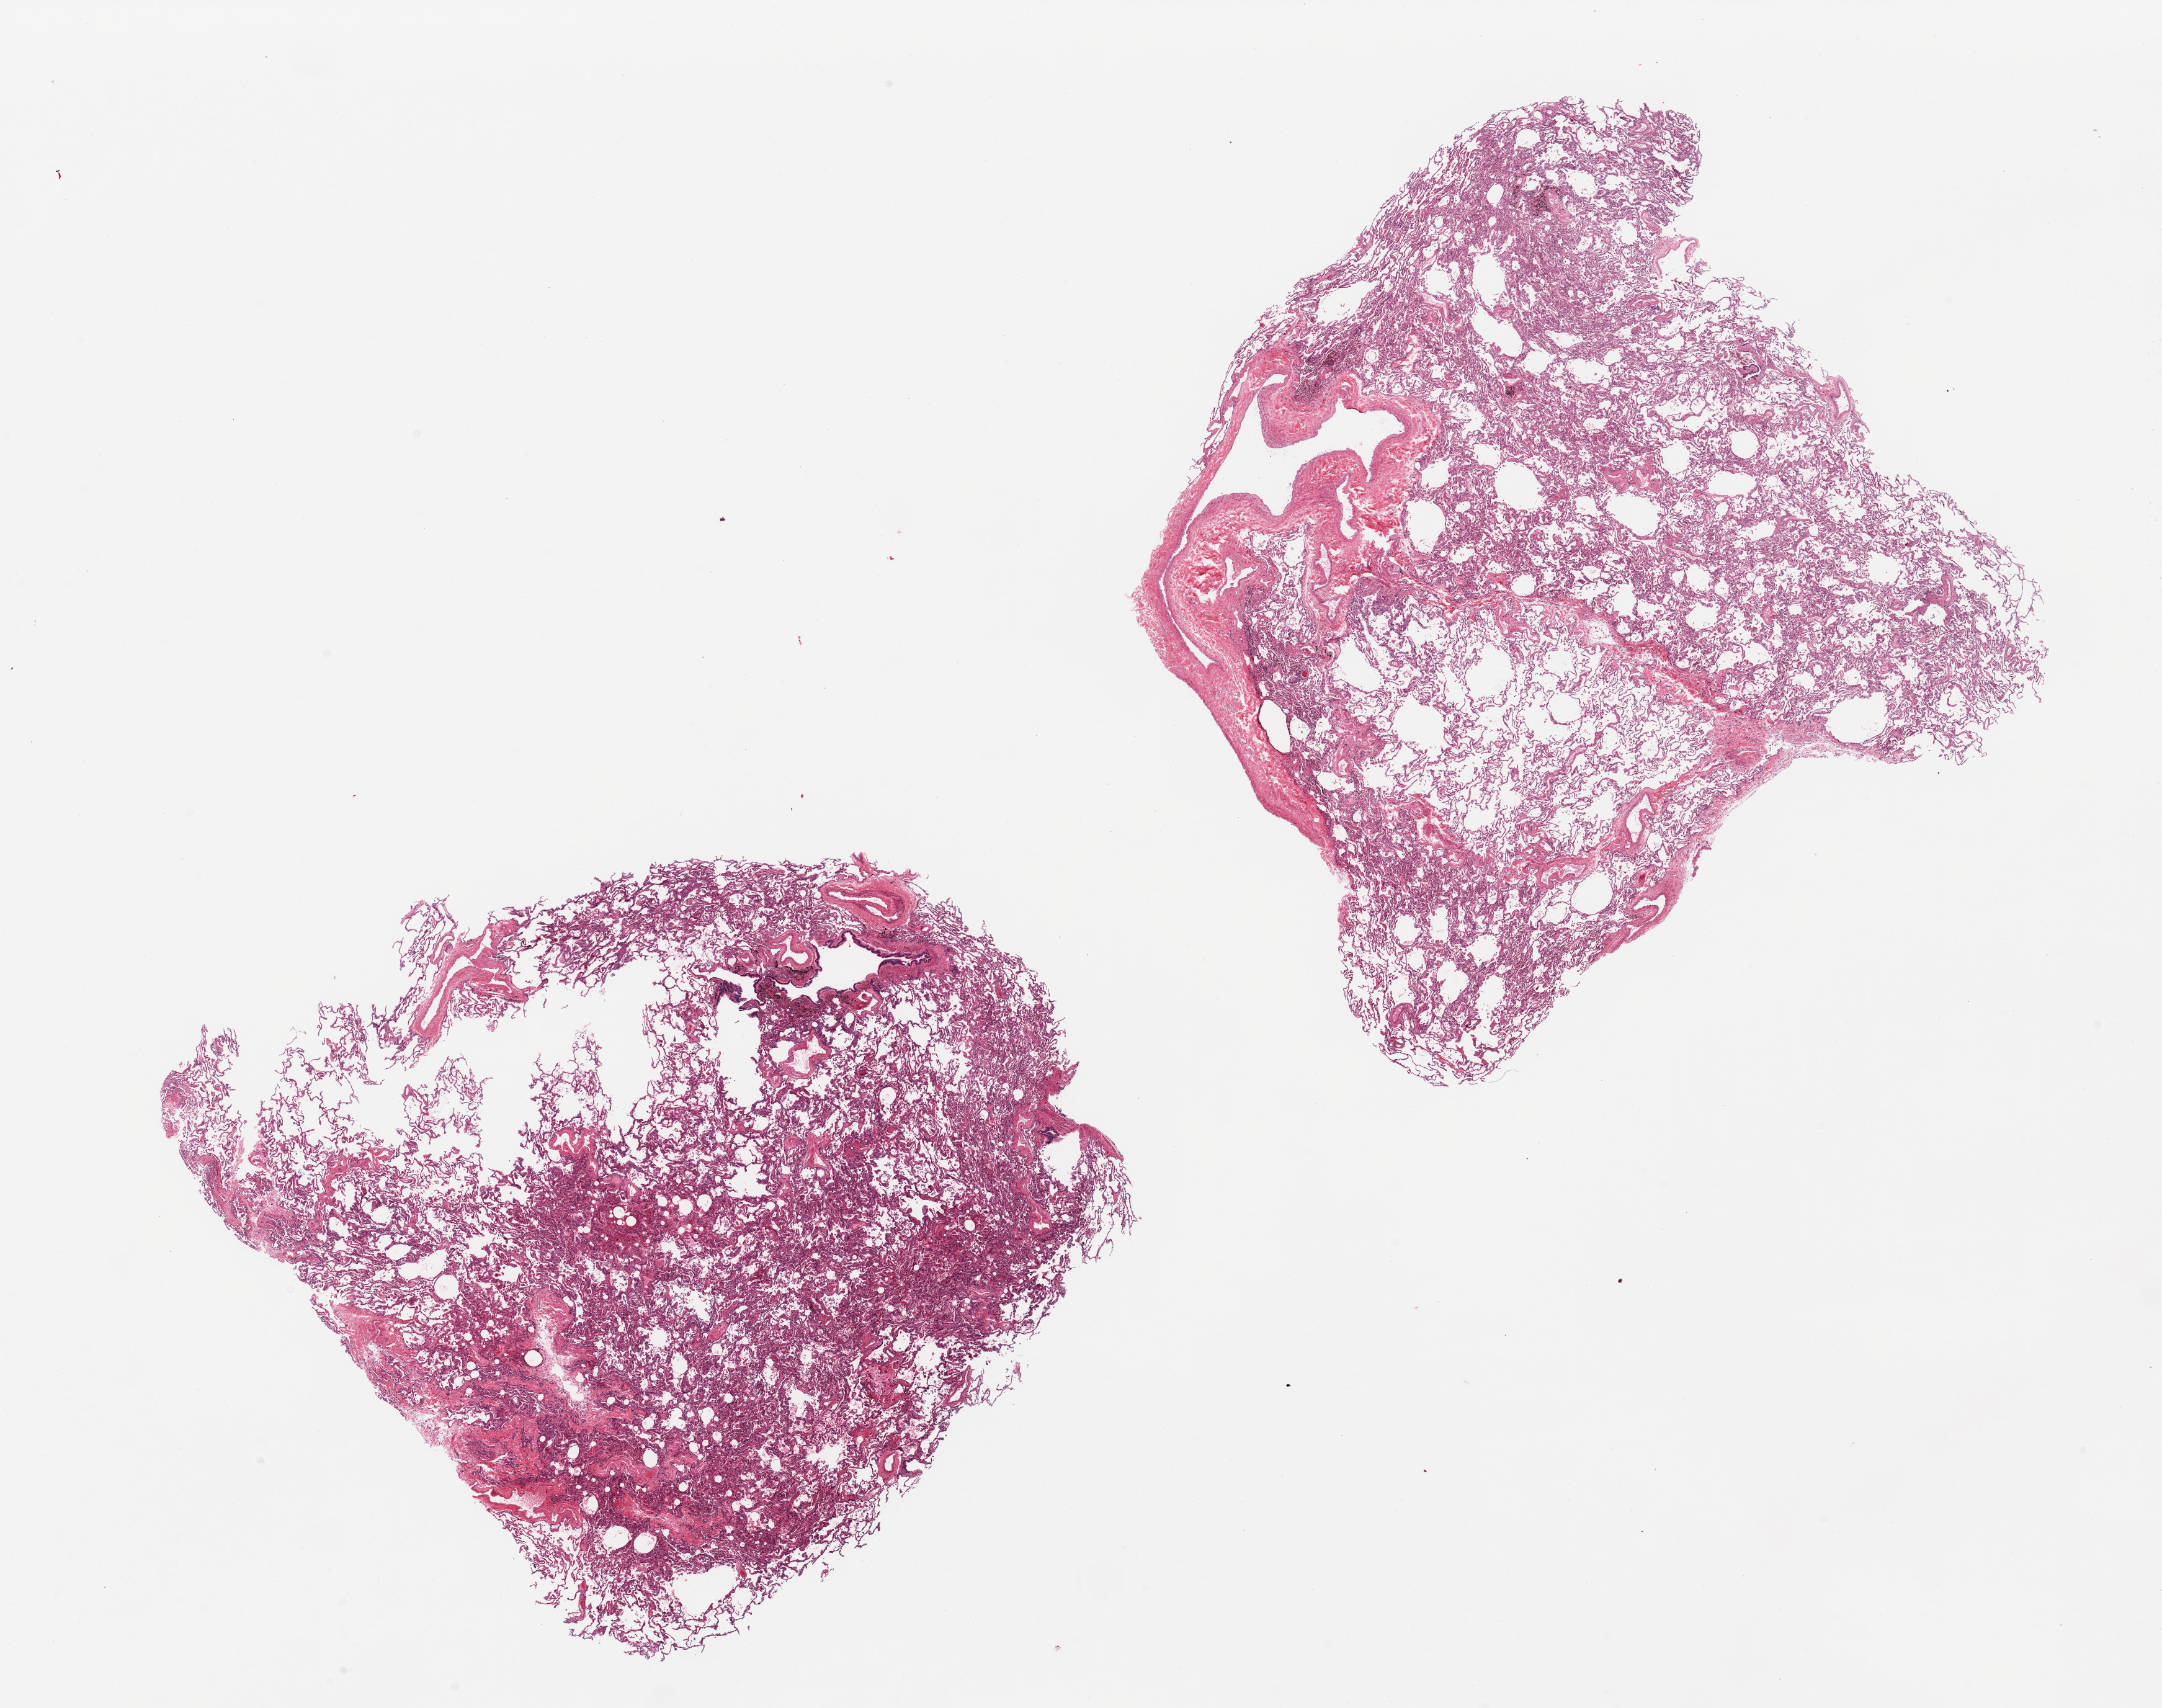
Whole-slide image, haematoxylin and eosin stain, brightfield — shown as a low-resolution overview of the whole scanned area (about 27.6 x 21.8 mm); PAXgene-fixed paraffin-embedded (PFPE) section; sampled site (target tissue): lung; tissue donor sample. Donor sex: male.
Review note (as recorded): 2 pieces; patchy pneumonia.